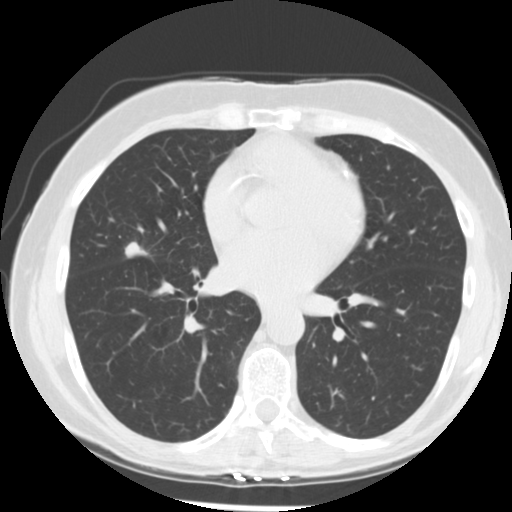
Low-dose screening chest CT, one axial slice; slice 129 of 255 in the series (ordered by position); reconstruction kernel STANDARD; 120 kVp; lung window (W 1500 / L -600 HU); 2.5 mm slice thickness; 512 × 512 image matrix, field of view 320 × 320 mm.
Outlined on this slice (outlined manually by an expert reader):
- lesion 1 (tumor, middle lobe of right lung): box from (x=125, y=242) to (x=146, y=258) px